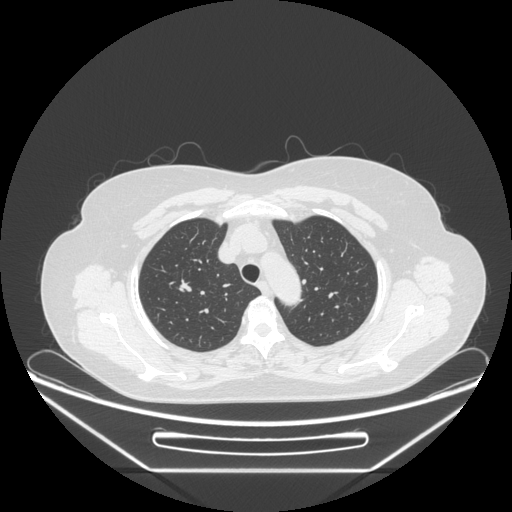
Chest CT, one axial slice. Slice 194 of 236 in the series (ordered by position). Reconstruction kernel STANDARD. Lung window (W 1500 / L -600 HU). 1.25 mm slice thickness. 512 × 512 image matrix, field of view 433 × 433 mm. Patient: female, 60 years. Case-level facts recorded for this patient, not image findings: clinical TNM (as recorded): T1c N0 M0.
Outlined on this slice (bounding box drawn by a radiologist):
- lung tumour (recorded histology: adenocarcinoma): bounding box (x1, y1, x2, y2) in pixels: (172, 271, 195, 296)